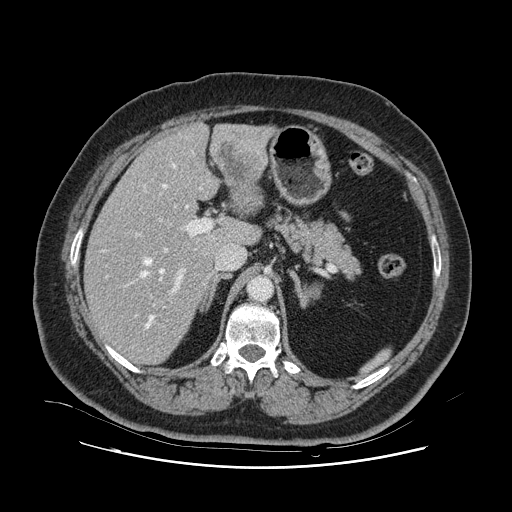
Contrast-enhanced abdominal CT, one axial slice; 120 kVp; intravenous contrast given; soft-tissue window (W 400 / L 40 HU); 2.5 mm slice thickness; 512 × 512 image matrix, field of view 391 × 391 mm. Female patient, age 73 years. Case-level facts recorded for this patient, not image findings: diagnosis: colorectal cancer liver metastases, imaged before liver resection; multiple liver metastases: no; largest metastasis: 7 cm.
Annotated regions visible in this slice (expert manual segmentation):
- hepatic veins: box from (x=101, y=164) to (x=221, y=328) px
- liver: (x=86, y=123)–(x=270, y=364)
- planned liver remnant (the part of the liver to remain after resection): (x=86, y=152)–(x=243, y=364)
- portal vein (with intrahepatic branches): (x=136, y=219)–(x=212, y=306)
- liver metastasis: (x=220, y=143)–(x=256, y=203)